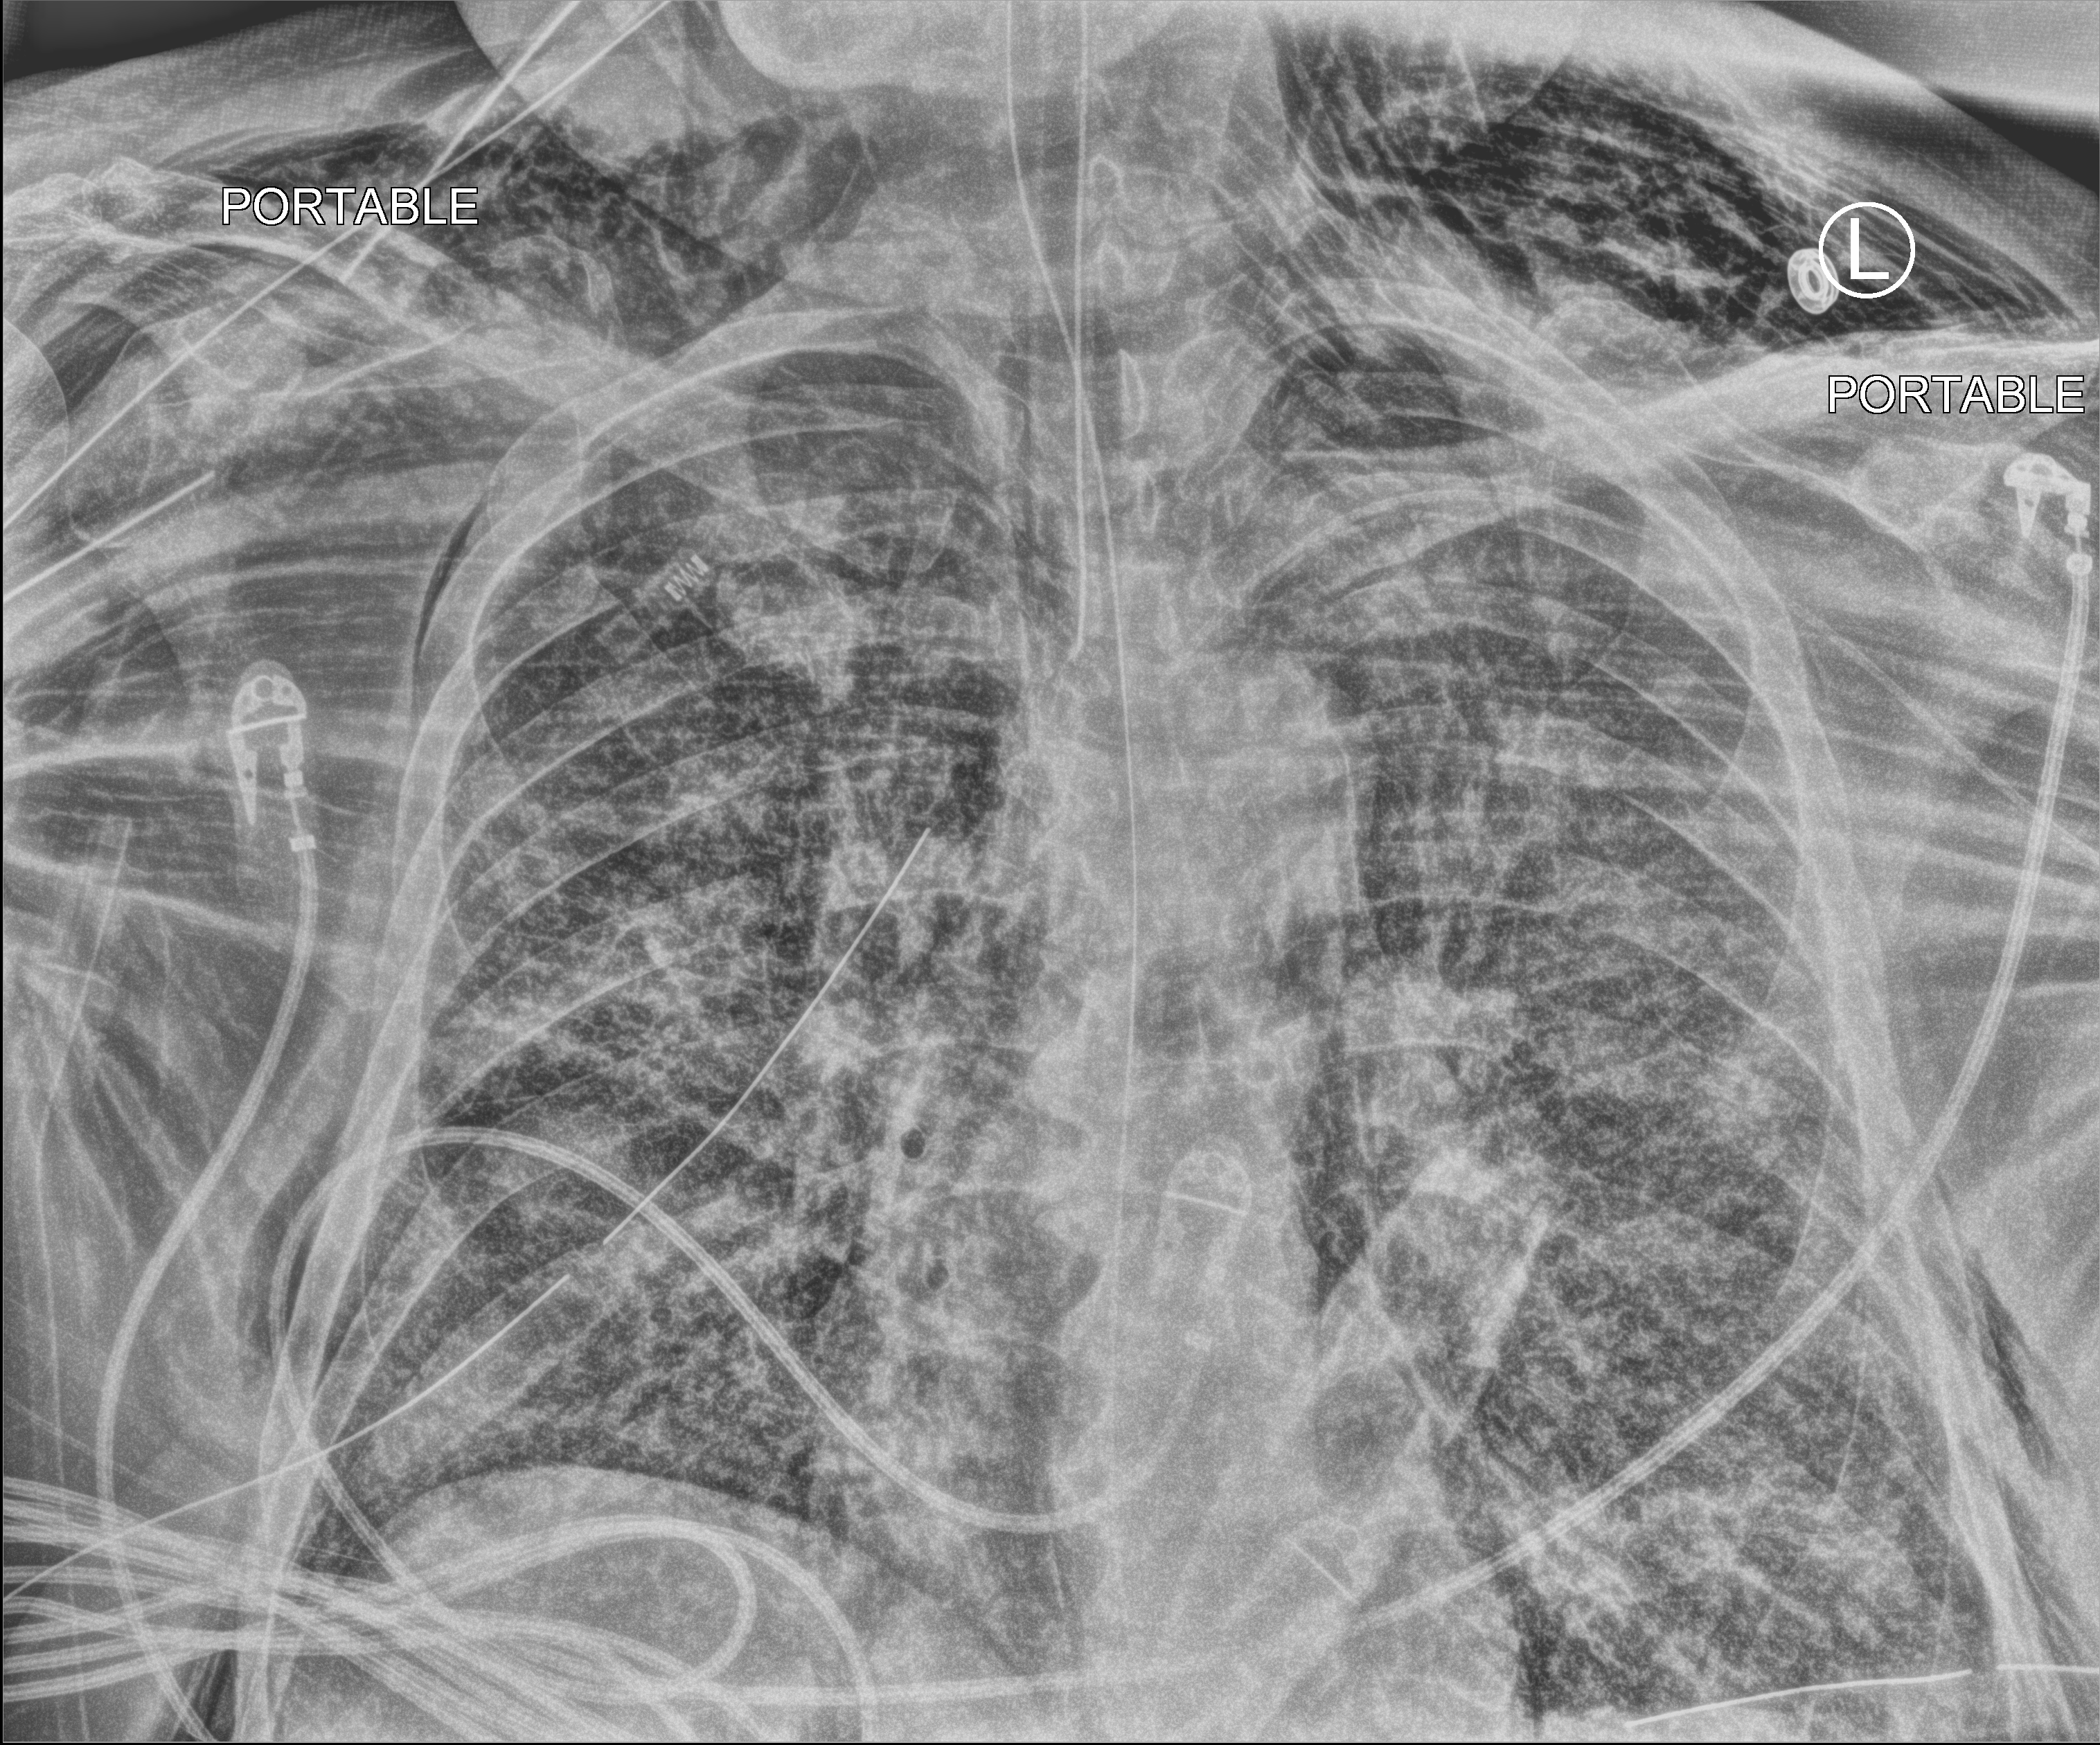
Bedside chest radiograph (computed radiography). Adult patient hospitalised with COVID-19, age 18–59 years.
Hospital-stay facts (about this admission, not read from this image; timing relative to this image not recorded):
- mechanically ventilated during this hospital stay: yes